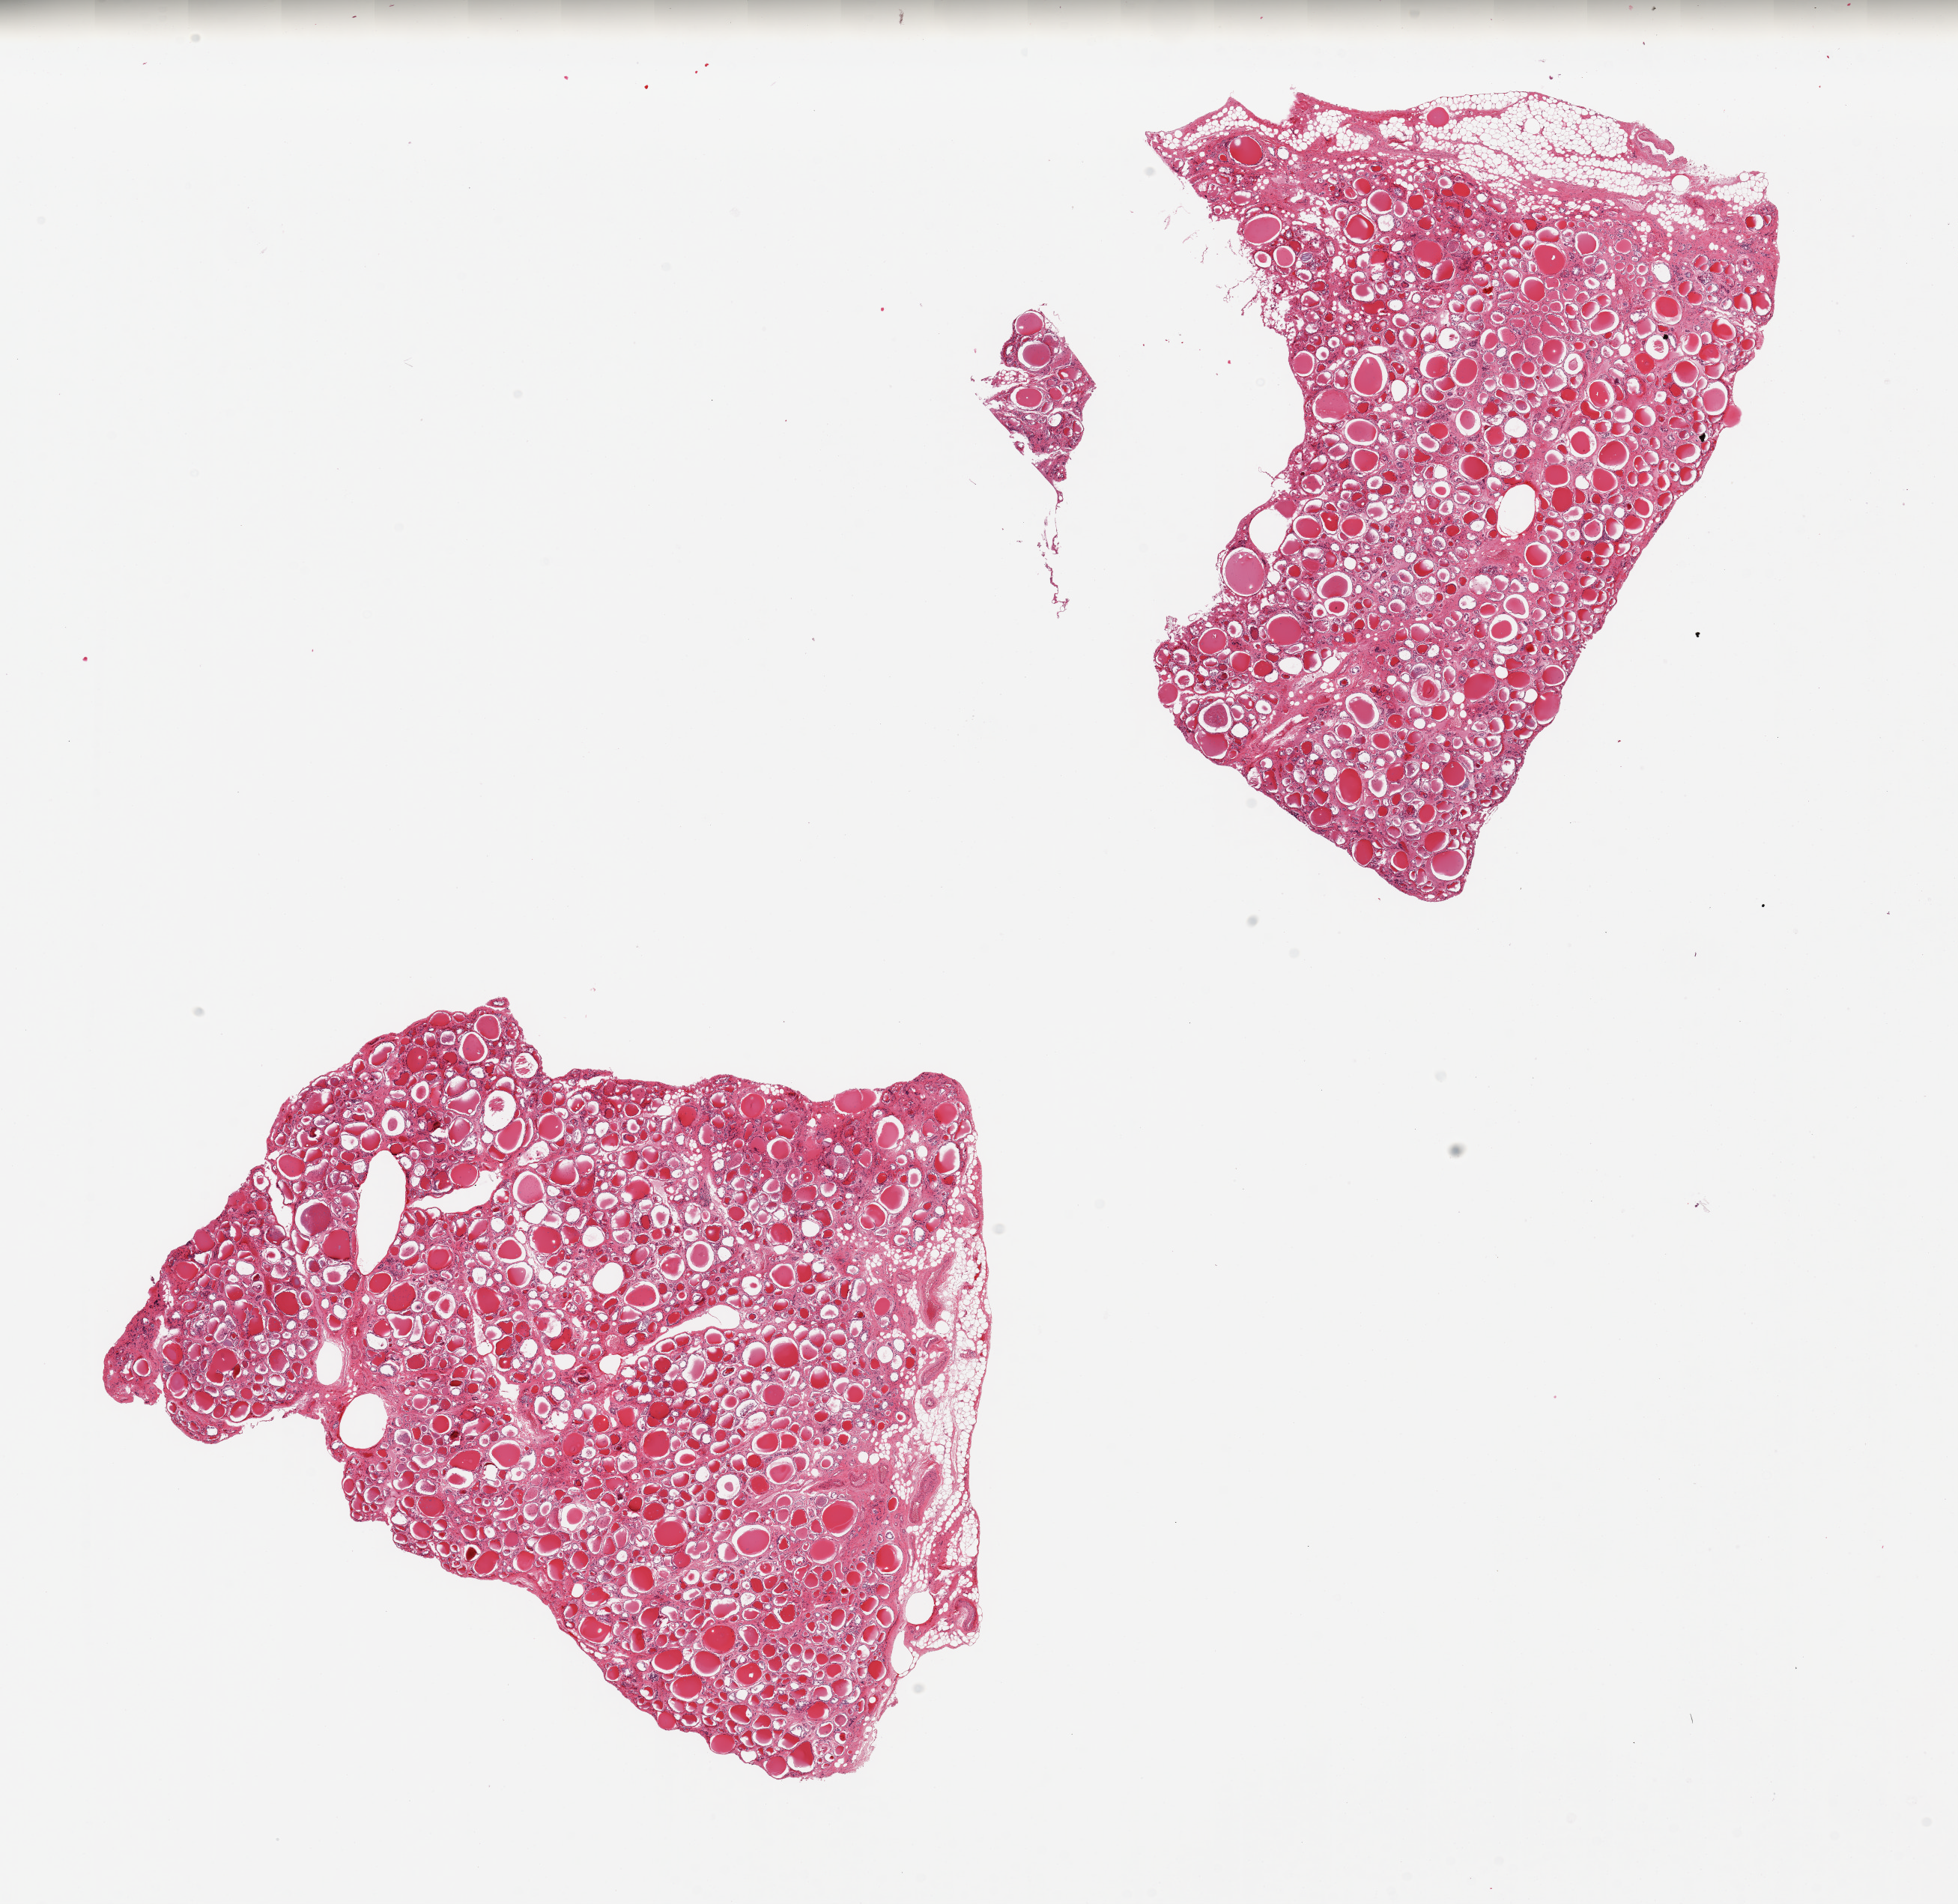
H&E whole-slide image — a low-resolution overview of the entire scanned area, about 20.7 x 20.1 mm (slide scanned at 20x), PAXgene-fixed, paraffin-embedded tissue, sampled site (target tissue): thyroid, donor tissue sample. Donor sex: male.
Pathologist's review note for this sample: 2 pieces, no significant findings, minimal aderhent fat.